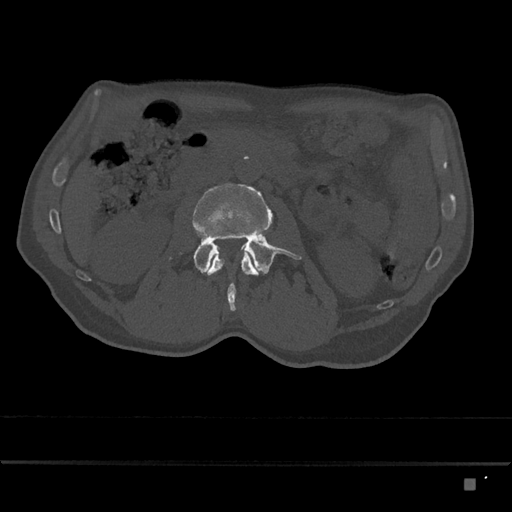
CT including the spine, one axial slice. Position 432 of 797 along the scan axis. 120 kVp. Bone window (W 1800 / L 400 HU). 0.5 mm slice thickness. 512 × 512 image matrix, field of view 390 × 390 mm. Male patient, age 72 years. From the clinical record (not read from this slice): primary cancer: prostate.
Annotated regions visible in this slice (semi-automatically segmented with operator editing):
- L2 vertebra: bounding box [x1, y1, x2, y2] px = [204, 252, 259, 312]
- L3 vertebra: [170, 183, 302, 274]